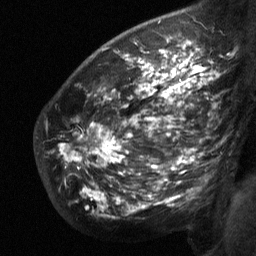
Breast MRI (dynamic contrast-enhanced), one sagittal slice; position 44 of 64 along the scan axis; dynamic contrast-enhanced study with each time point stored as its own series, time point 2 of 3 at this slice position (early post-contrast, ordered by acquisition time); 1.5 T; TE 4.8 ms, TR 27 ms; 2 mm slice thickness; 256 × 256 image matrix. Female patient, age 50 years. From the clinical record (not read from this slice): setting: breast cancer imaged before/during neoadjuvant chemotherapy; receptor status: HER2-positive.
Annotated regions visible in this slice (semi-automatically segmented with operator editing):
- analysis volume of interest (the breast-tissue region the enhancement analysis was run in; not a lesion): bounding box <61,62,213,206> (left, top, right, bottom; pixels)
- tumour enhancement mask (voxels above the 90 % enhancement threshold inside the analysis volume of interest): <72,62,210,201>